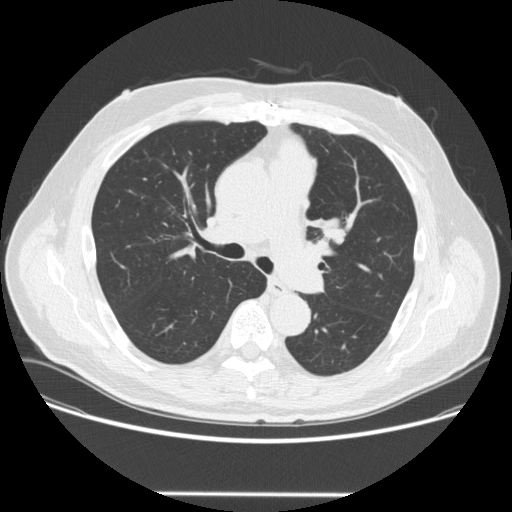
Low-dose screening chest CT, one axial slice. Lung window (W 1500 / L -600 HU). 512 × 512 image matrix, field of view 400 × 400 mm.
Structures marked on this image (manually delineated by an expert):
- lesion 1 (tumor, upper lobe of left lung): box from (x=321, y=221) to (x=343, y=242) px